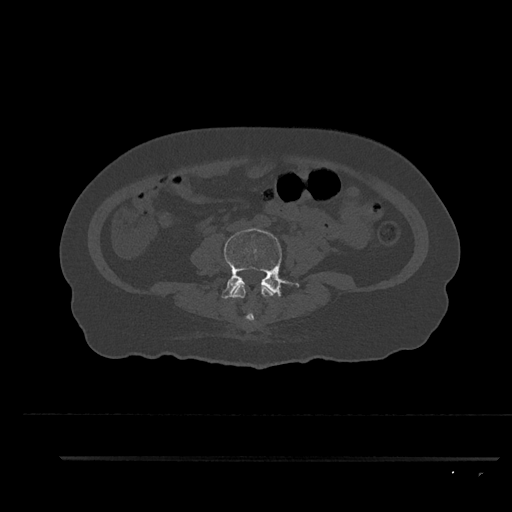
CT including the spine, one axial slice. Position 41 of 797 along the scan axis. 120 kVp. Bone window (W 1800 / L 400 HU). 0.5 mm slice thickness. 512 × 512 image matrix, field of view 408 × 408 mm. Patient: female, 44 years. From the clinical record (not read from this slice): primary cancer: renal.
Structures marked on this image (semi-automatically segmented with operator editing):
- L3 vertebra: bounding box (x1, y1, x2, y2) in pixels: (232, 285, 280, 320)
- L4 vertebra: (221, 228, 300, 299)